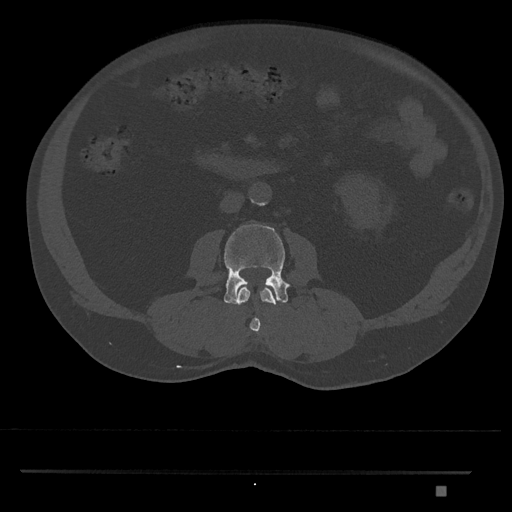
CT including the spine, one axial slice. Slice 705 of 1134 in the series (ordered by position). 120 kVp. Bone window (W 1800 / L 400 HU). 0.5 mm slice thickness. 512 × 512 image matrix. Patient: male, 65 years. From the clinical record (not read from this slice): primary cancer: prostate.
Structures marked on this image (semi-automatically segmented with operator editing):
- L2 vertebra: bounding box <237,287,277,334> (left, top, right, bottom; pixels)
- L3 vertebra: <224,224,291,305>